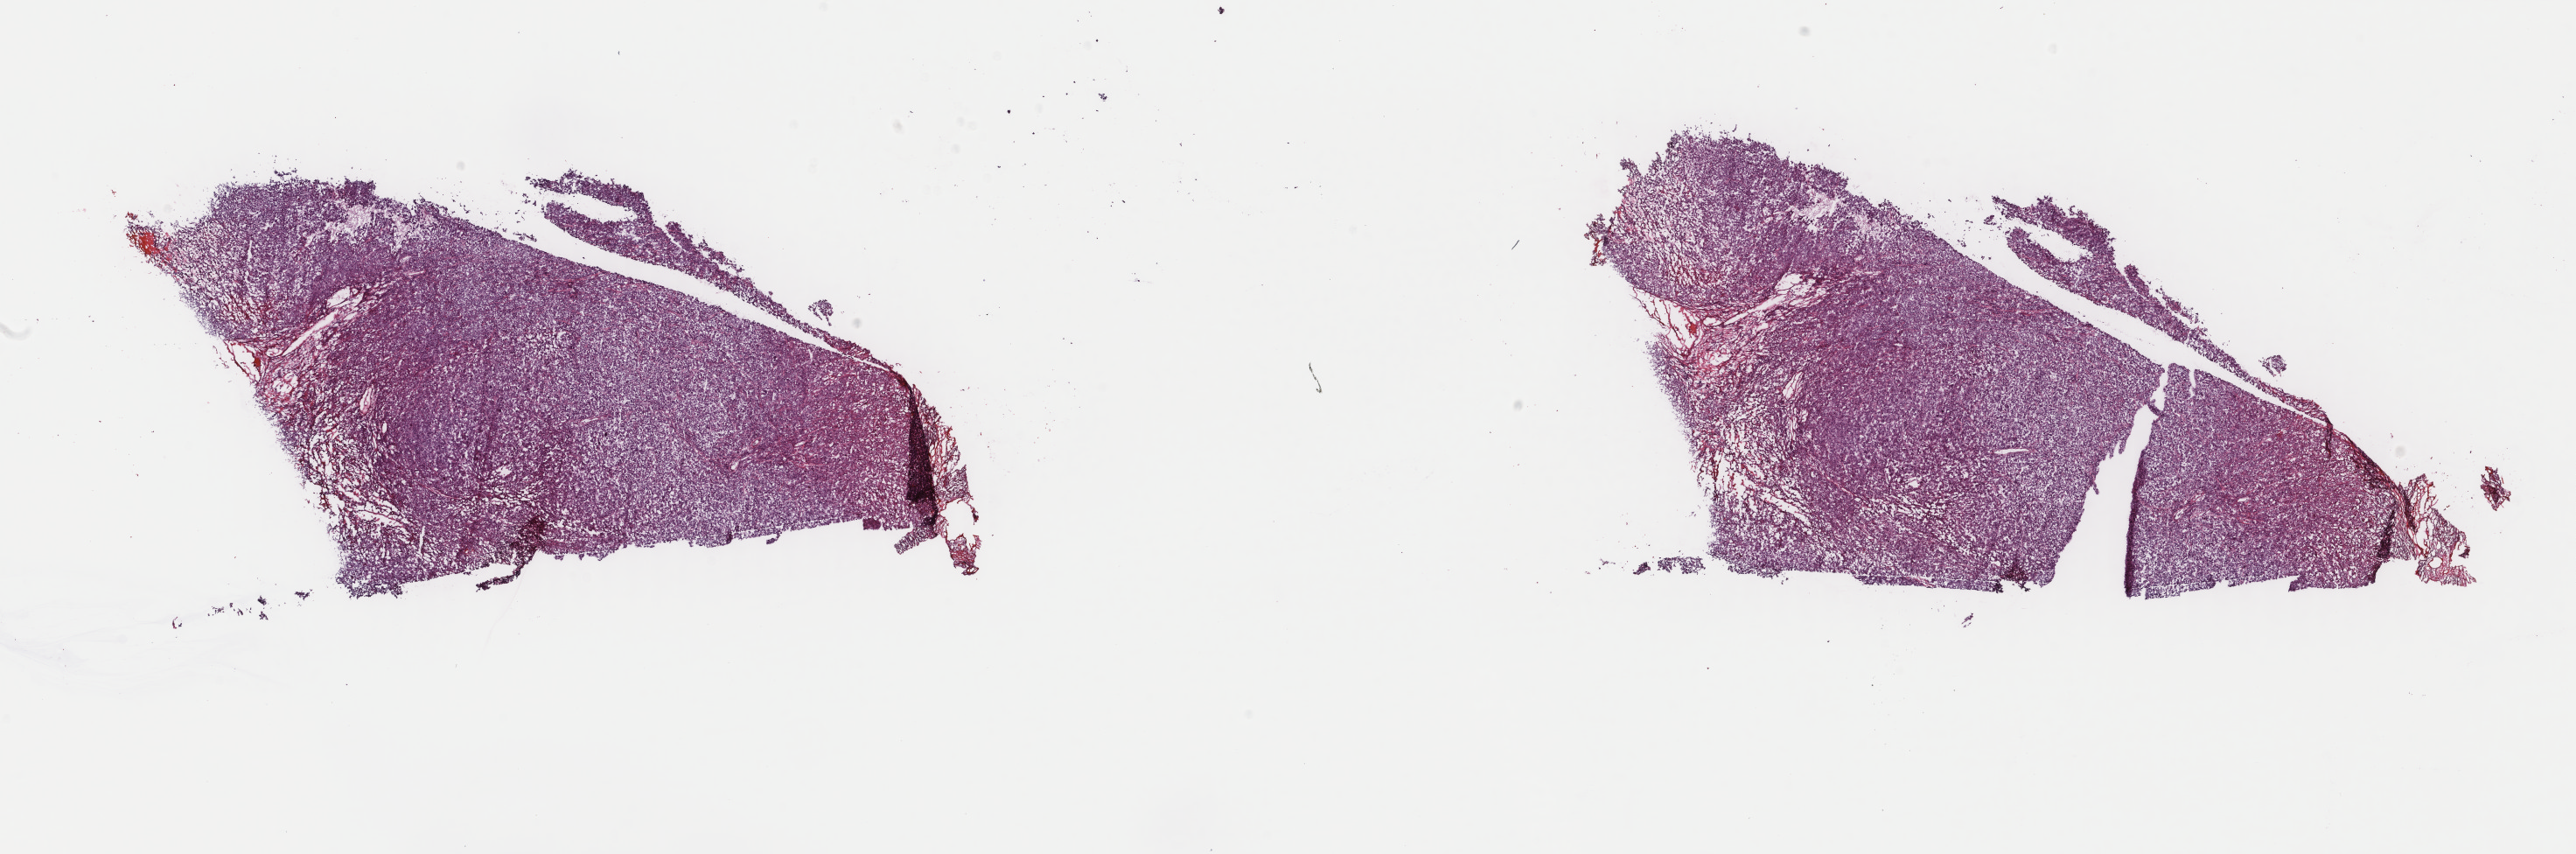
Digitized Hematoxylin and eosin (H&E) stained tissue section (whole slide), a low-resolution overview of the entire scanned area, about 23.4 x 7.7 mm (acquisition: 40x scan). Frozen section from the top of the tissue portion. Head and neck, primary tumour sample. Male, age 73 years at initial diagnosis. Histologic grade: G3 (poorly differentiated). Slide review estimates, as recorded: tumour cells 100%, tumour nuclei 75%, normal cells 0%, stromal cells 0%, necrosis 0%. Inflammatory infiltration, as recorded: lymphocyte infiltration 9%, monocyte infiltration 0%, neutrophil infiltration 1%.
Diagnosis: Squamous cell carcinoma, NOS. AJCC pathologic stage: II.